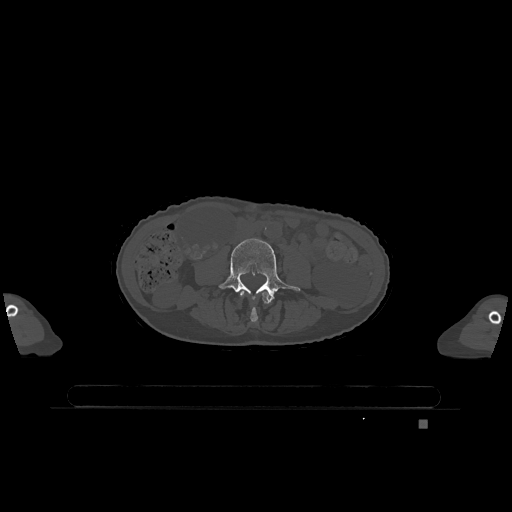
CT including the spine, one axial slice; slice 307 of 1317 in the series (ordered by position); bone window (W 1800 / L 400 HU); 0.5 mm slice thickness; 512 × 512 image matrix, field of view 500 × 500 mm. Female patient, age 74 years. Case-level facts recorded for this patient, not image findings: primary cancer: lung; vertebrae with lytic lesions (as recorded): T1, T4, T5, T6, L4, L5.
Outlined on this slice (semi-automatically segmented with operator editing):
- L3 vertebra: bounding box <240,290,271,323> (left, top, right, bottom; pixels)
- L4 vertebra: <218,238,300,301>